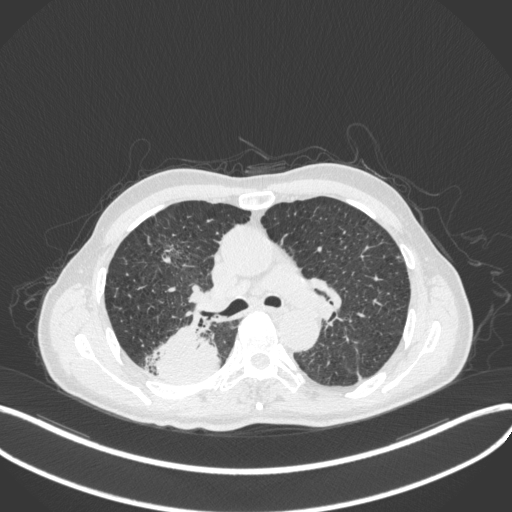
Chest CT, one axial slice; position 289 of 423 along the scan axis; reconstruction kernel B31f; 120 kVp; lung window (W 1500 / L -600 HU); 1 mm slice thickness; 512 × 512 image matrix, field of view 400 × 400 mm. Male patient, age 79 years. From the clinical record (not read from this slice): clinical TNM (as recorded): T3 N0 M0.
Structures marked on this image (rectangle marked by the reading radiologist):
- lung tumour (recorded histology: adenocarcinoma): box from (x=152, y=319) to (x=223, y=386) px